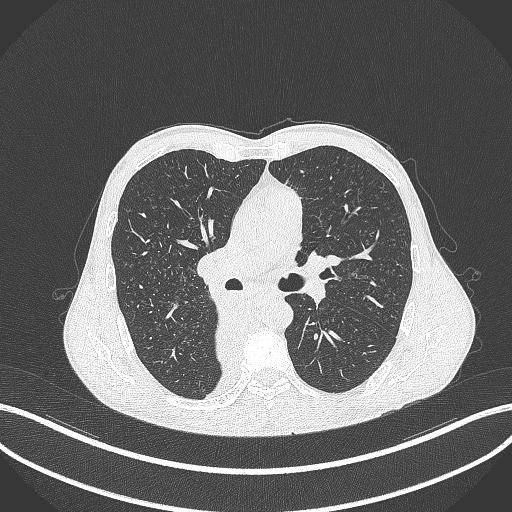
Chest CT, one axial slice; slice 222 of 371 in the series (ordered by position); reconstruction kernel B70f; lung window (W 1500 / L -600 HU); 512 × 512 image matrix, field of view 400 × 400 mm. Male patient, age 58 years. Case-level facts recorded for this patient, not image findings: clinical TNM (as recorded): T3 N1 M1.
Annotated regions visible in this slice (bounding box drawn by a radiologist):
- lung tumour (recorded histology: squamous cell carcinoma): bounding box (x1, y1, x2, y2) in pixels: (209, 290, 251, 362)